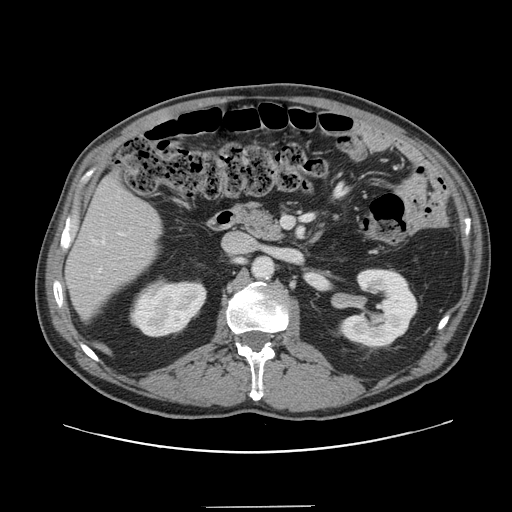
Contrast-enhanced abdominal CT, one axial slice; position 66 of 139 along the scan axis; 120 kVp; soft-tissue window (W 400 / L 40 HU); 2.5 mm slice thickness; 512 × 512 image matrix, field of view 397 × 397 mm. Male patient, age 64 years. Case-level facts recorded for this patient, not image findings: diagnosis: colorectal cancer liver metastases, imaged before liver resection; multiple liver metastases: yes; largest metastasis: 3.5 cm.
Outlined on this slice (expert manual segmentation):
- hepatic veins: box from (x=99, y=241) to (x=105, y=271) px
- liver: (x=67, y=179)–(x=161, y=318)
- planned liver remnant (the part of the liver to remain after resection): (x=67, y=179)–(x=161, y=318)
- portal vein (with intrahepatic branches): (x=119, y=232)–(x=124, y=235)